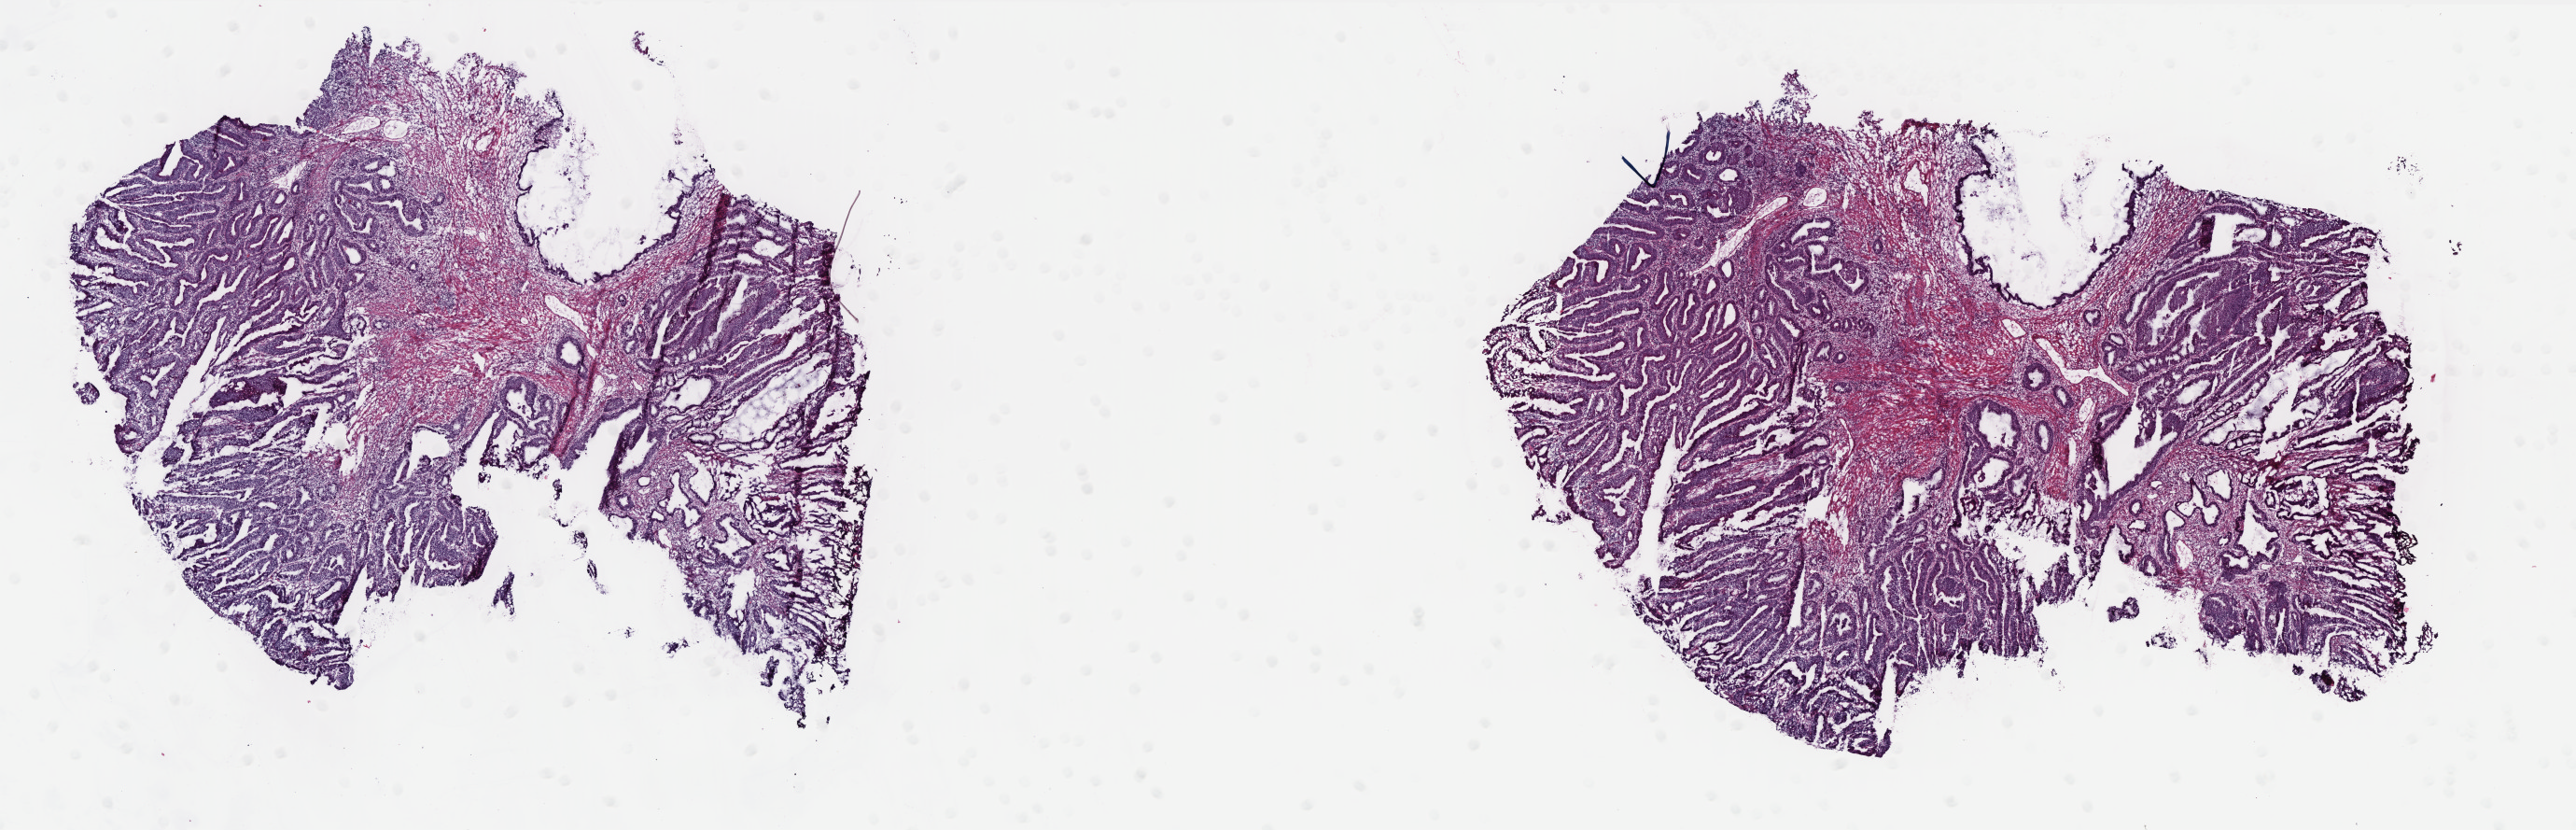
H&E whole-slide image — whole scanned area (about 22.1 x 7.1 mm, acquisition: 40x scan) shown as a low-resolution overview; frozen section; rectum, primary tumour sample. Patient: female, age at initial diagnosis 64 years. Pathologist review of this section (percent, as recorded): tumour cells 60%, tumour nuclei 60%, normal cells 30%, stromal cells 9%, necrosis 1%. Infiltration values recorded for this section: lymphocyte infiltration 10%, monocyte infiltration 1%, neutrophil infiltration 0%.
* AJCC pathologic stage: I (6th edition)
* lymph nodes positive (case pathology): 0 of 18 examined
* histologic diagnosis: Adenocarcinoma, NOS
* TNM: T1 N0 M0